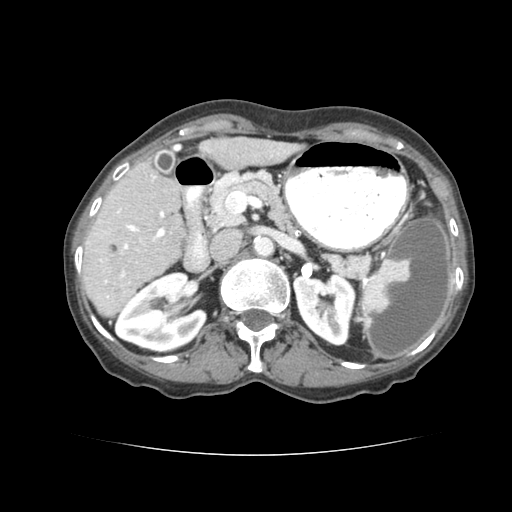
Contrast-enhanced abdominal CT (liver protocol), one axial slice; reconstruction kernel STANDARD; soft-tissue window (W 400 / L 40 HU); 512 × 512 image matrix. From the clinical record (not read from this slice): diagnosis: hepatocellular carcinoma (patient treated with transarterial chemoembolisation; whether this scan precedes or follows treatment is not stated here); TNM stage (as recorded): Stage-I; Child-Pugh class: A; tumour differentiation: well differentiated; tumour nodularity: uninodular.
Annotated regions visible in this slice (semi-automatically segmented with operator editing):
- liver parenchyma outside the tumour (the mass and vessels are separate outlines, so this box may not span the whole liver): bounding box <80,138,300,316> (left, top, right, bottom; pixels)
- liver vessels: <94,204,166,290>